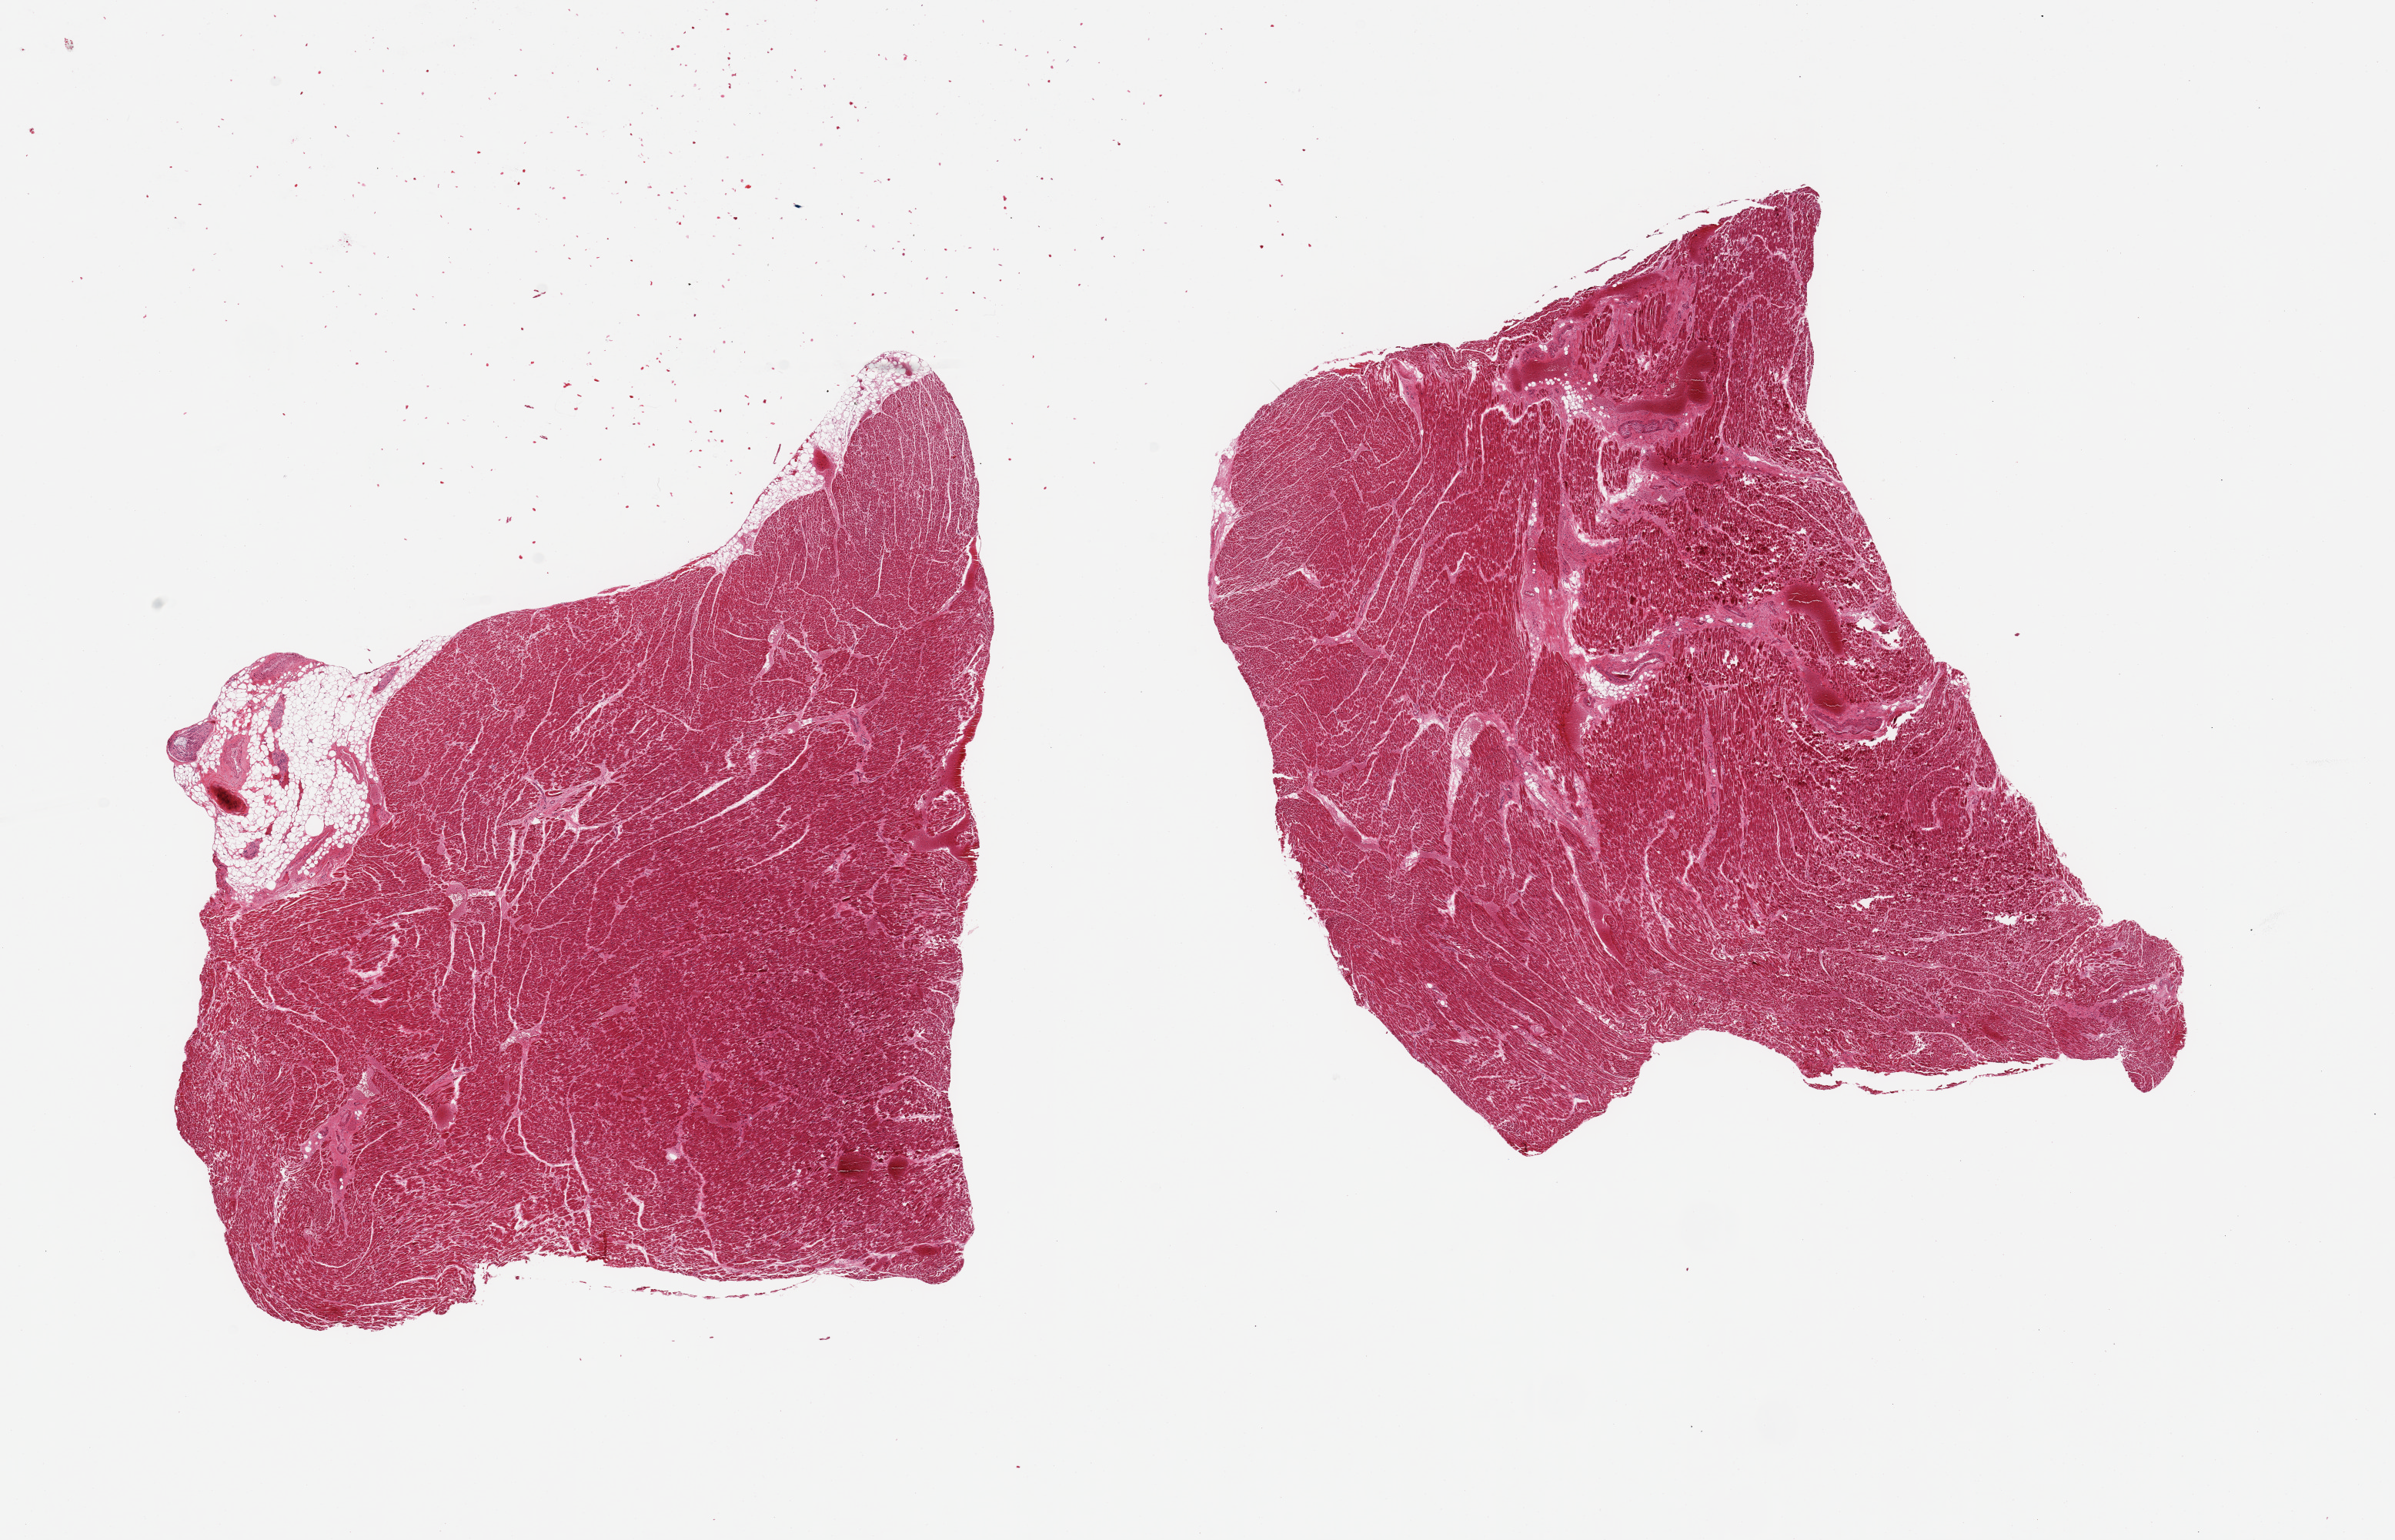
Digitized H&E-stained section — shown as a low-resolution overview of the whole scanned area (about 24.6 x 15.8 mm, acquisition: 20x scan). PAXgene-fixed paraffin-embedded (PFPE) section. Section of heart (target tissue). Donor tissue sample. Donor sex: male.
Reviewer comment on this tissue sample: 2 pieces. 1 with 10% external fat.